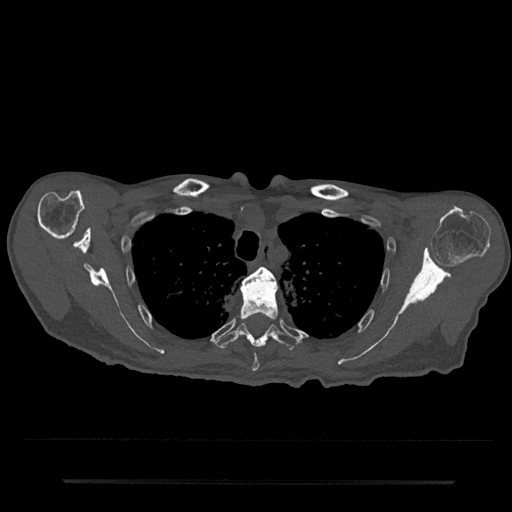
CT including the spine, one axial slice. Position 606 of 797 along the scan axis. 120 kVp. Bone window (W 1800 / L 400 HU). 512 × 512 image matrix. Patient: male, 74 years. Case-level facts recorded for this patient, not image findings: primary cancer: prostate.
Annotated regions visible in this slice (semi-automatic segmentation, software-assisted and operator-edited):
- T3 vertebra: bounding box (x1, y1, x2, y2) in pixels: (244, 267, 276, 282)
- T4 vertebra: (239, 275, 279, 372)
- T5 vertebra: (214, 322, 300, 350)